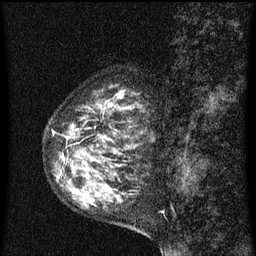
Breast MRI (dynamic contrast-enhanced), one sagittal slice. Slice 24 of 60 in the series (ordered by position). Dynamic contrast-enhanced series, image 2 of 3 at this slice position (ordered by acquisition). 1.5 T. TE 4.2 ms, TR 8 ms. 2 mm slice thickness. 256 × 256 image matrix, field of view 180 × 180 mm. Patient: female, 55 years.
Structures marked on this image (semi-automatically segmented with operator editing):
- analysis volume of interest (the breast-tissue region the enhancement analysis was run in; not a lesion): bounding box <48,88,159,151> (left, top, right, bottom; pixels)
- tumour enhancement mask (voxels above the 70 % enhancement threshold inside the analysis volume of interest): <66,94,131,149>